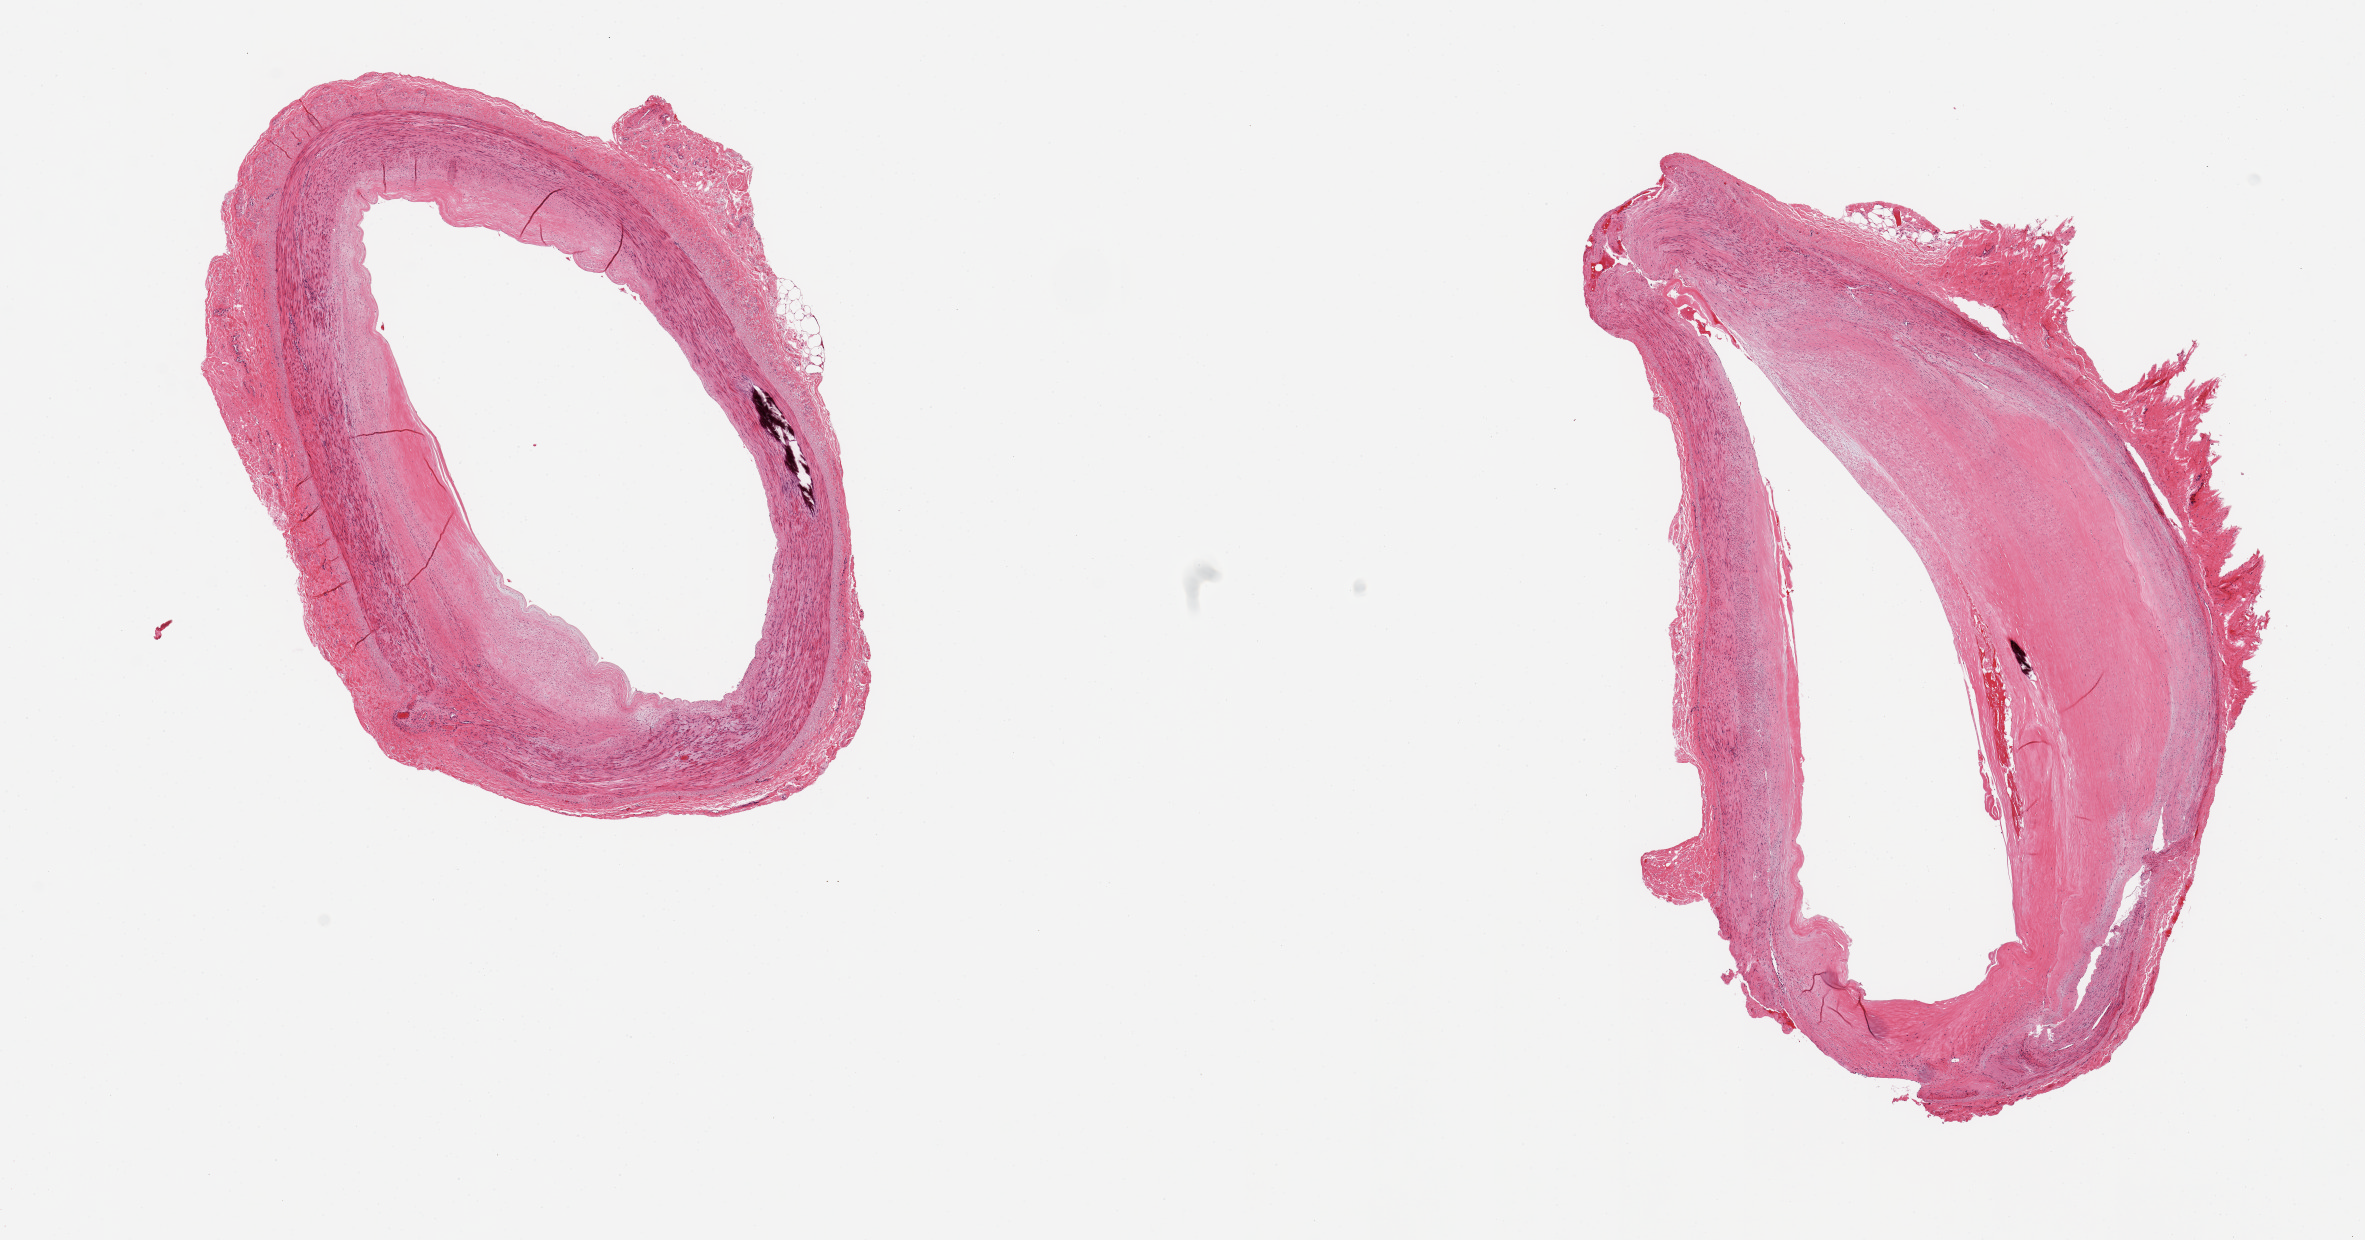
Hematoxylin and eosin (H&E) whole-slide image — shown as a low-resolution overview of the whole scanned area (about 18.7 x 9.8 mm, from a 20x scan); PAXgene-fixed, paraffin-embedded tissue; target tissue: tibial artery; tissue donor sample. Donor: male.
Review note (as recorded): 2 pieces, ~50% occlusive atherosis; focal Monckberg medial sclerosis.